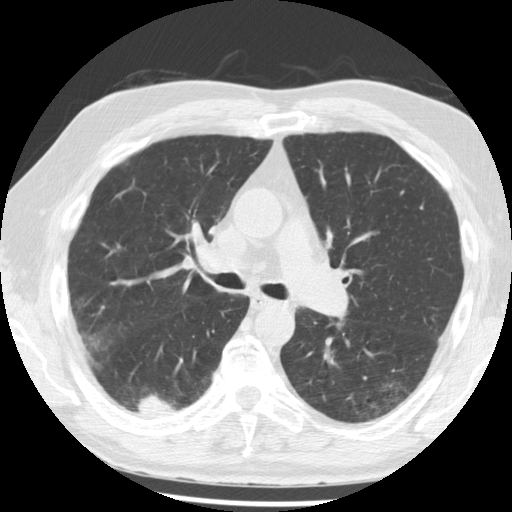
Low-dose screening chest CT, one axial slice. Position 127 of 221 along the scan axis. Lung window (W 1500 / L -600 HU). 2.5 mm slice thickness. 512 × 512 image matrix, field of view 350 × 350 mm.
Annotated regions visible in this slice (outlined manually by an expert reader):
- lesion 1 (tumor, lower lobe of right lung): bounding box (x1, y1, x2, y2) in pixels: (135, 395, 180, 417)